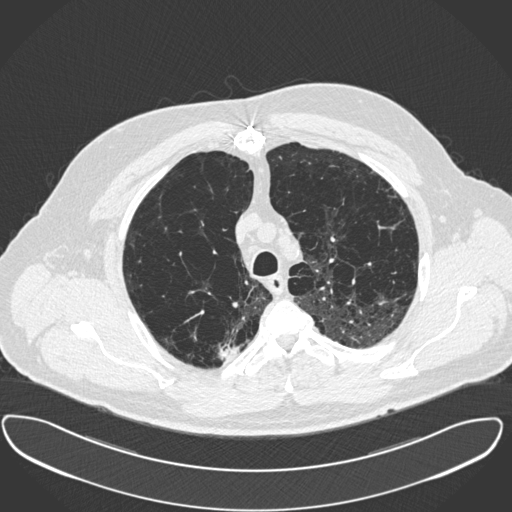
Low-dose screening chest CT, one axial slice. Slice 306 of 385 in the series (ordered by position). Reconstruction kernel B30f. Lung window (W 1500 / L -600 HU). 1 mm slice thickness. 512 × 512 image matrix, field of view 408 × 408 mm.
Annotated regions visible in this slice (manually delineated by an expert):
- lesion 1 (tumor, upper lobe of right lung): bounding box [x1, y1, x2, y2] px = [218, 344, 239, 361]